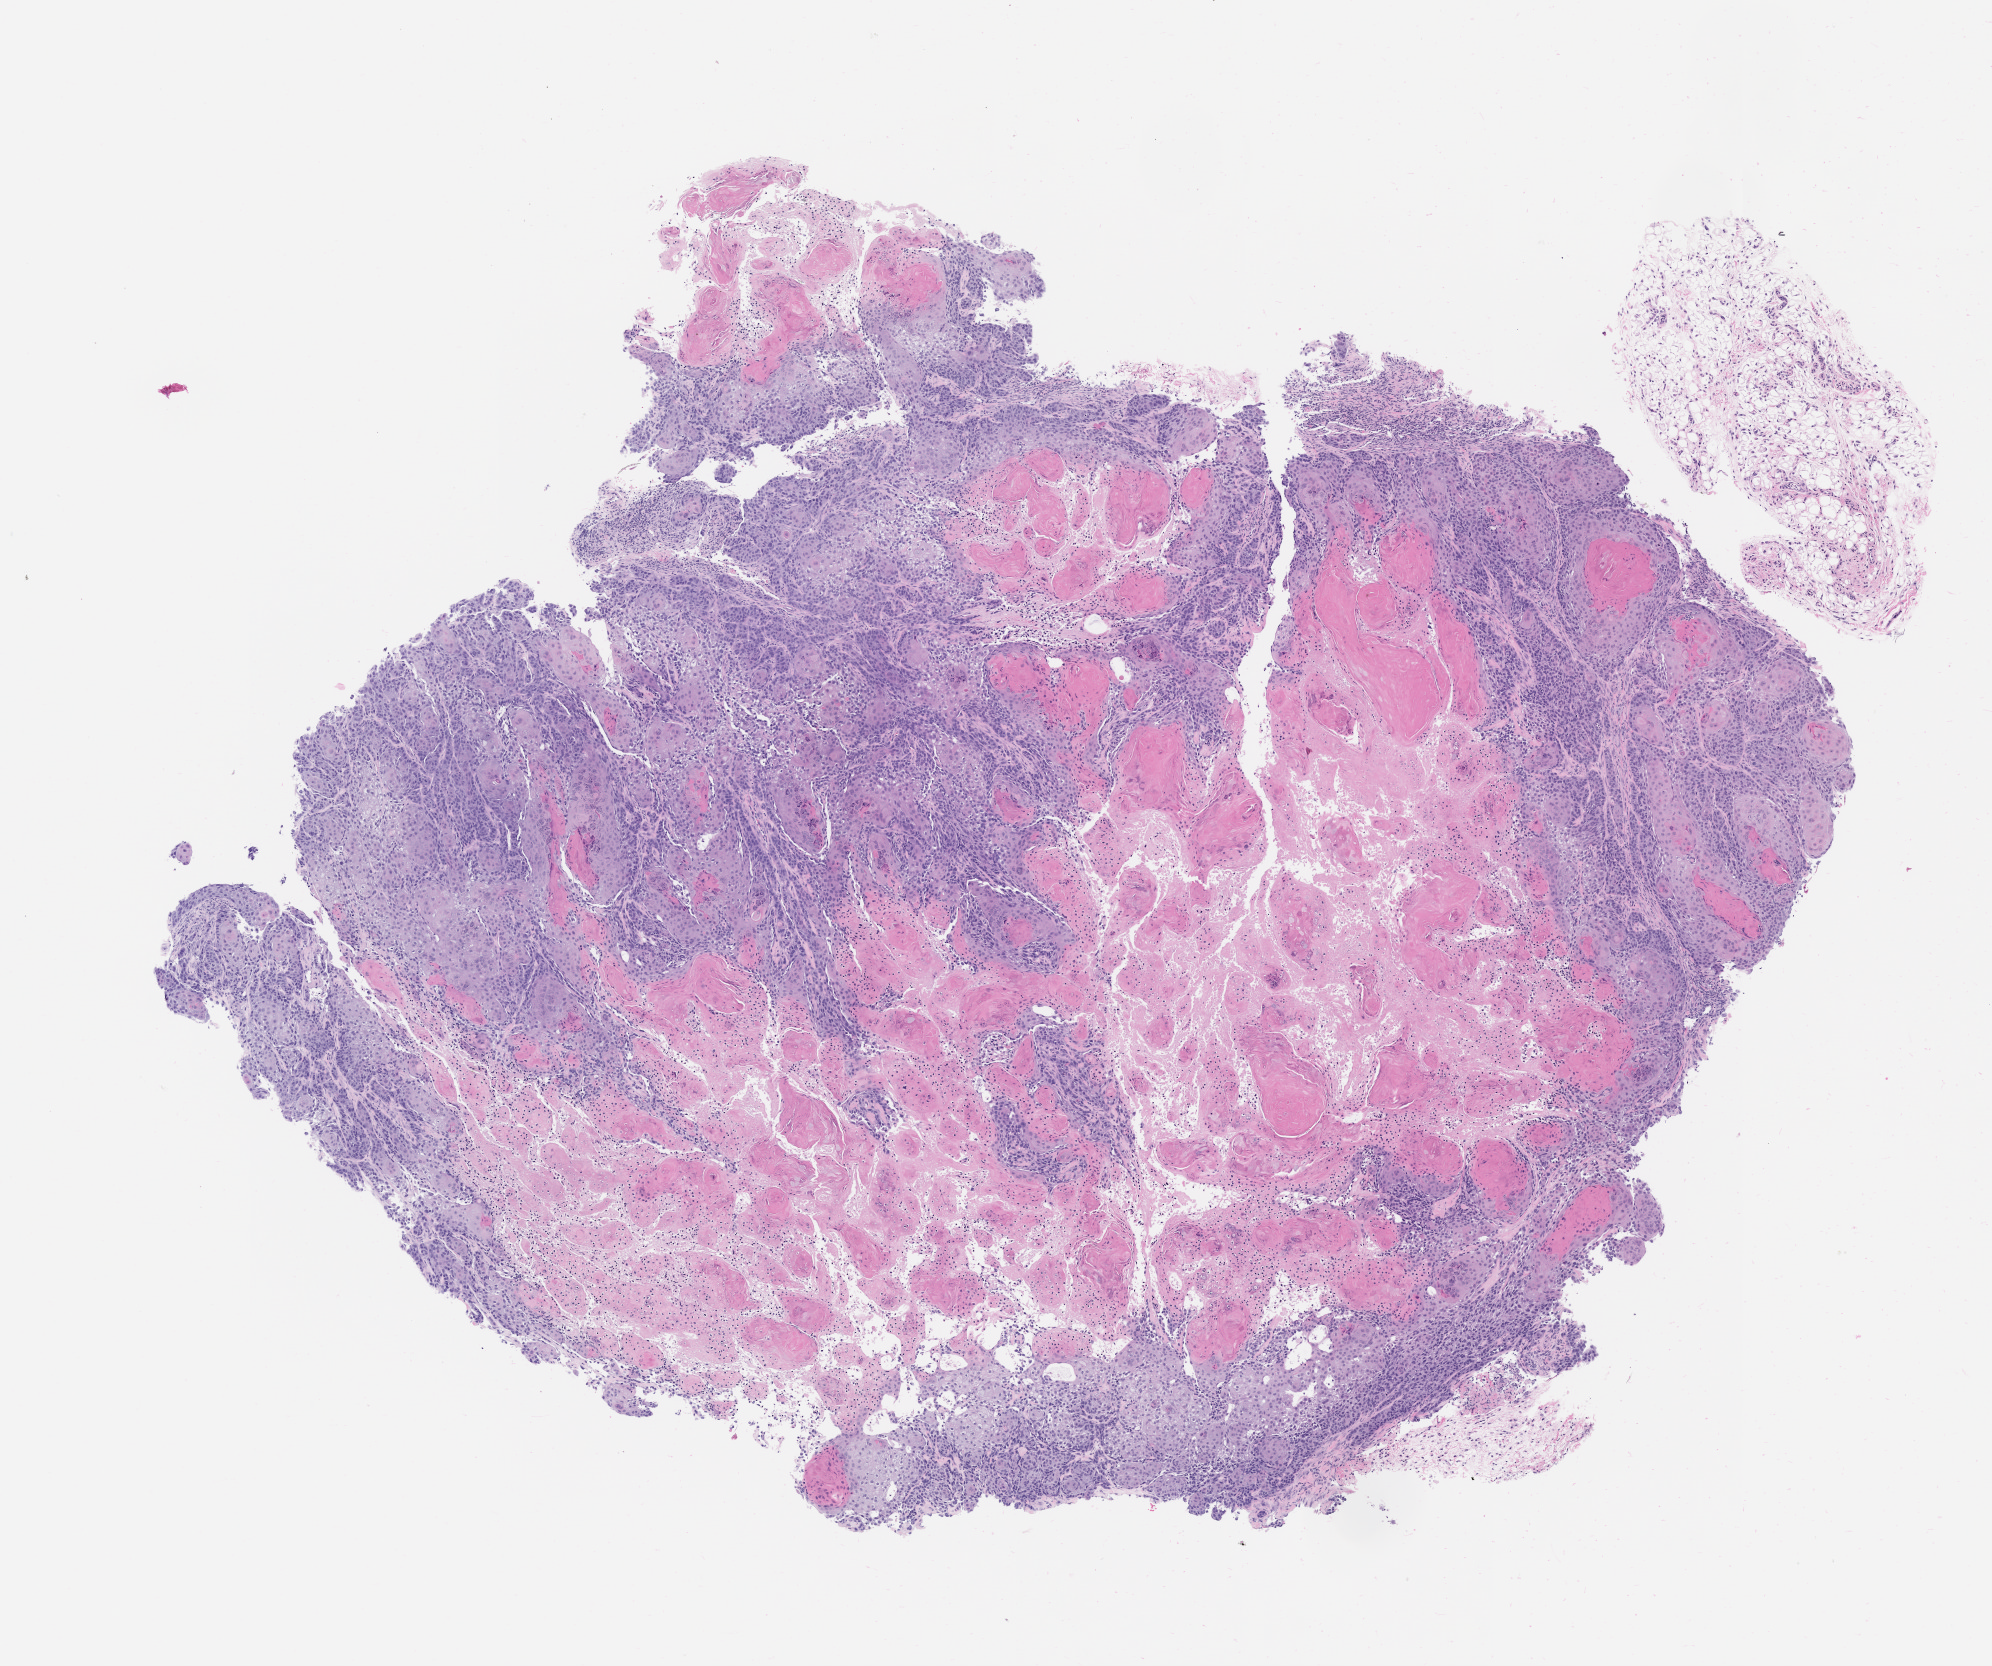
H&E whole-slide image of a patient-derived xenograft (PDX) tumor grown in a mouse, passage 1, low-resolution overview of the scanned area, about 8.0 x 6.7 mm, formalin-fixed, paraffin-embedded (FFPE) tissue, tumor site category: oral soft tissue.
Originating patient diagnosis: Head and Neck Squamous Cell Carcinoma.